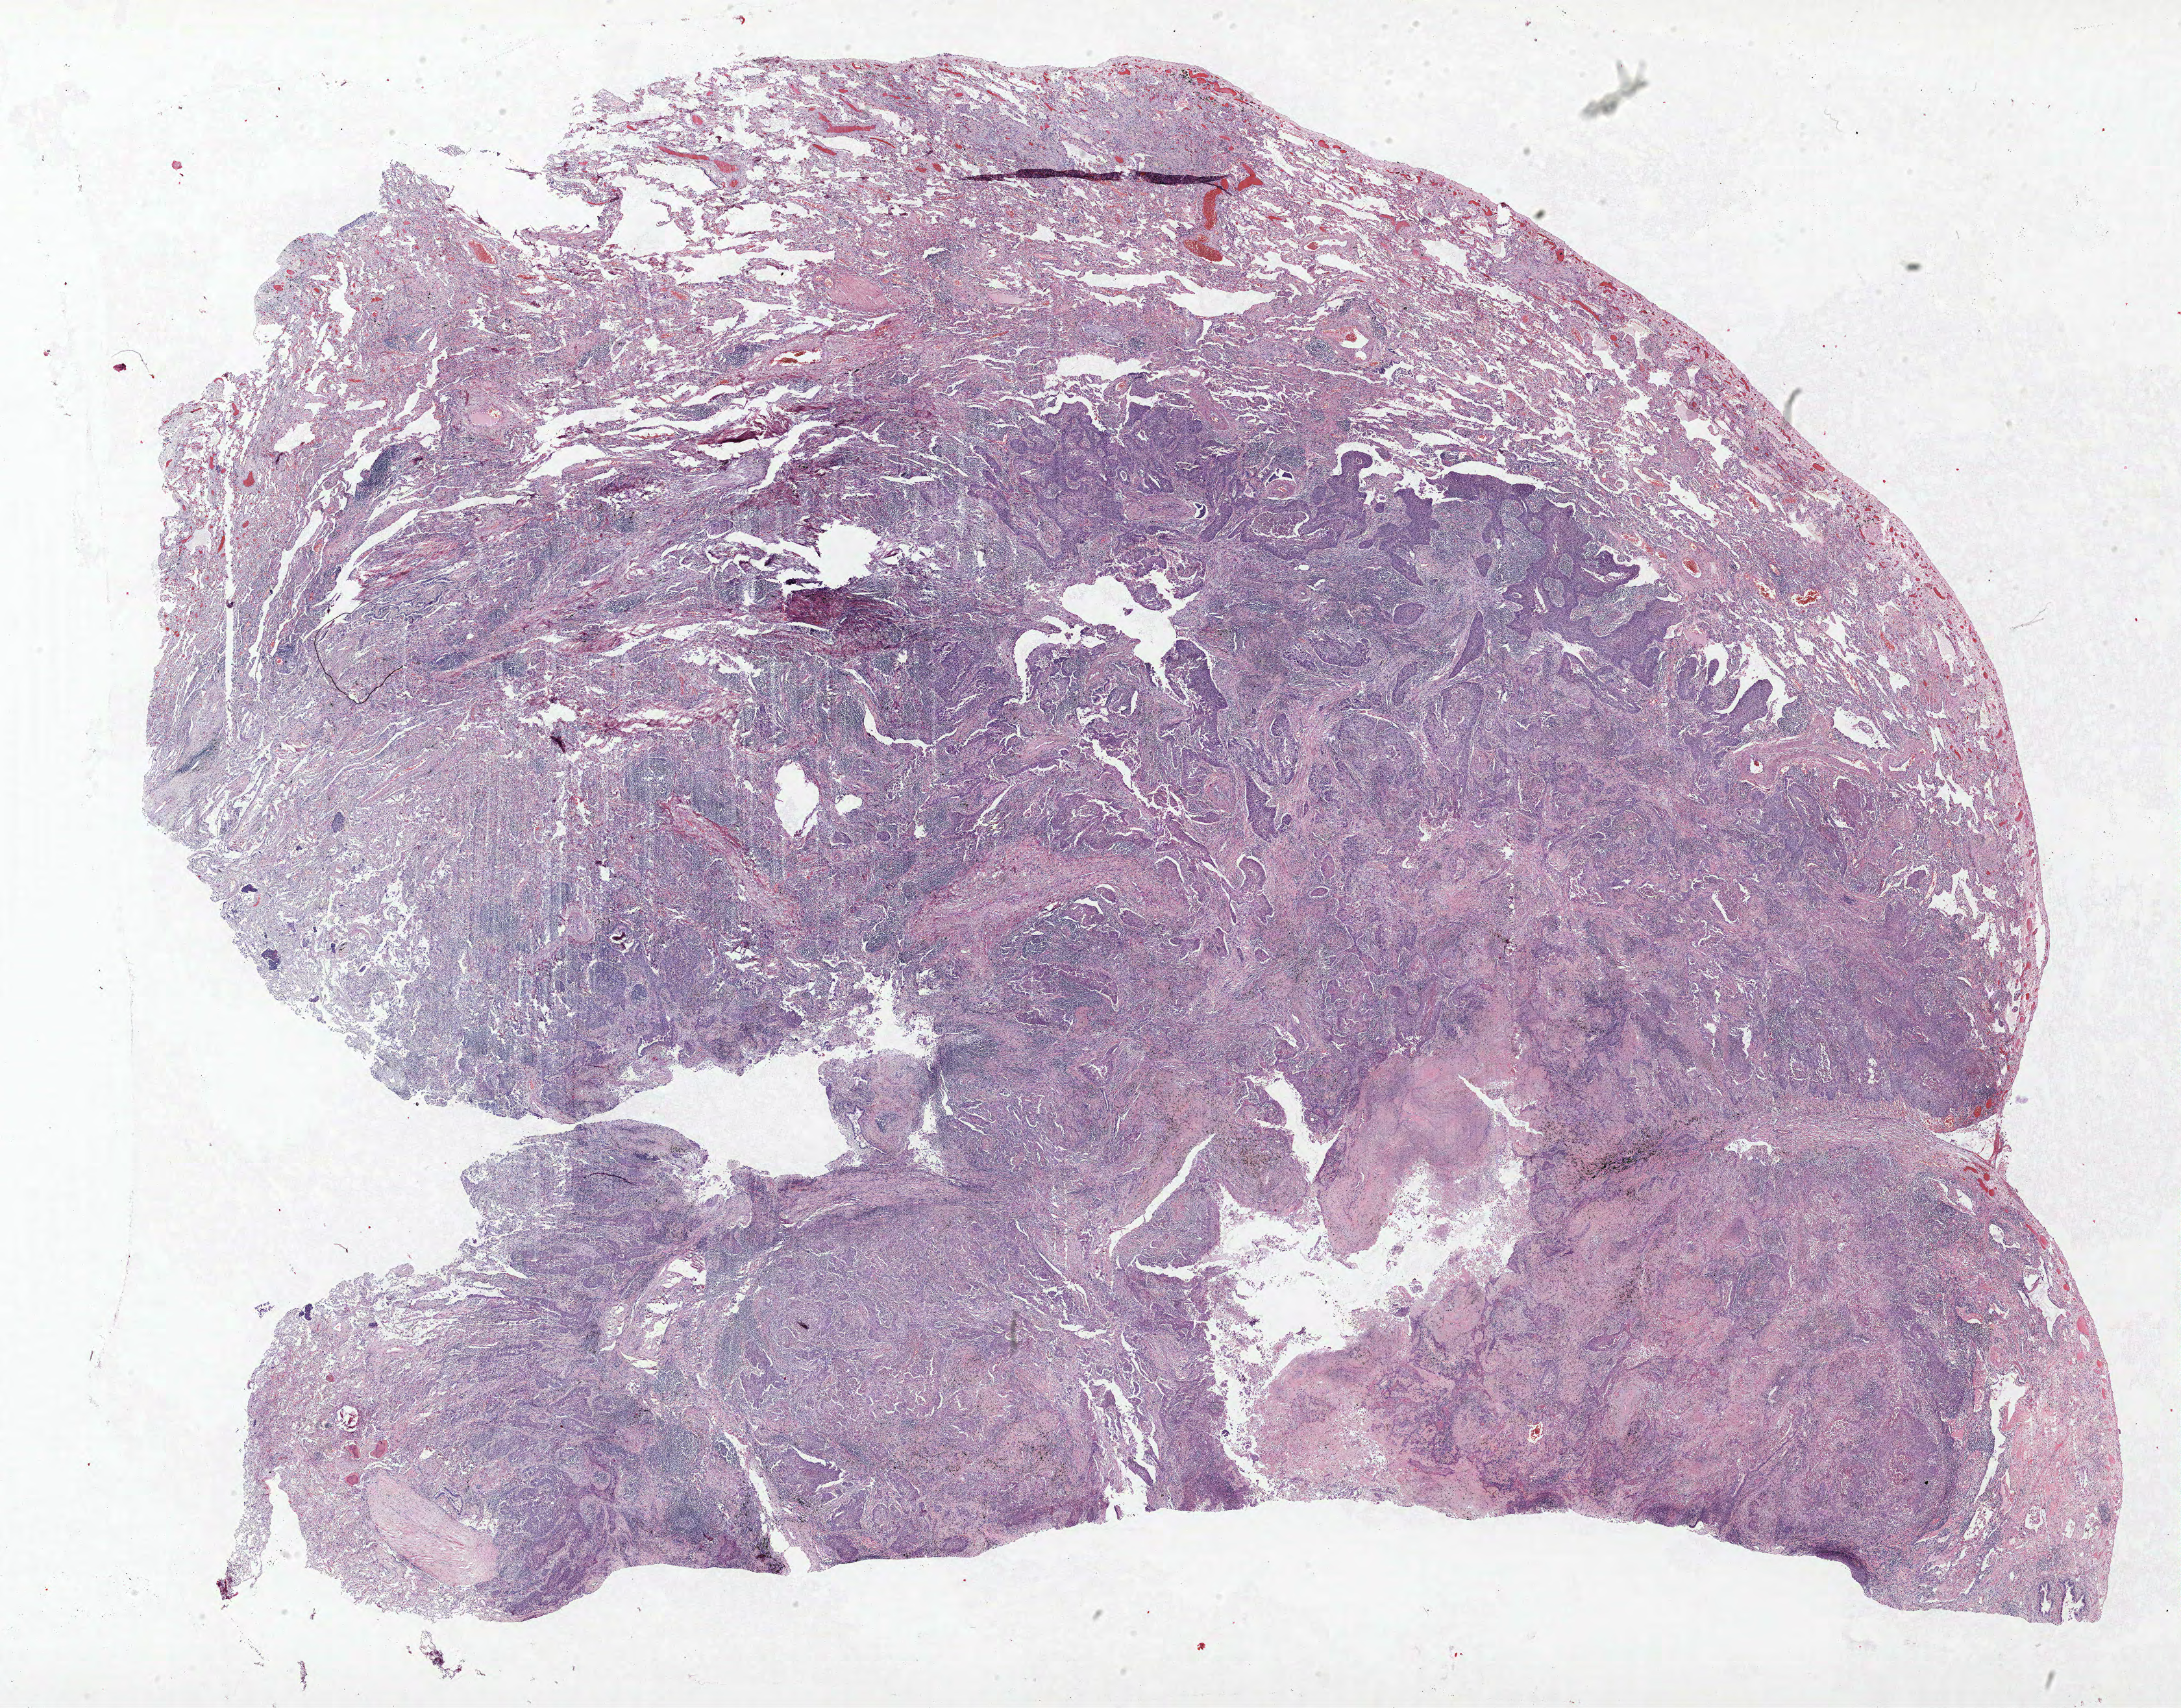
Whole-slide histology image, Hematoxylin and eosin (H&E) stained — shown as a low-resolution overview of the whole scanned area (about 26.9 x 21.1 mm), FFPE section, lung. Male patient, aged 68 at enrolment. Former smoker at enrolment. Grade: poorly differentiated (G3).
Tumour size (pathology): 30 mm. Primary tumour location (clinical record): right lower lobe. ICD-O-3 topography: lower lobe of lung (C34.3). Participant's lung-cancer diagnosis: Adenosquamous carcinoma. Stage (AJCC 6th edition): IIIA.